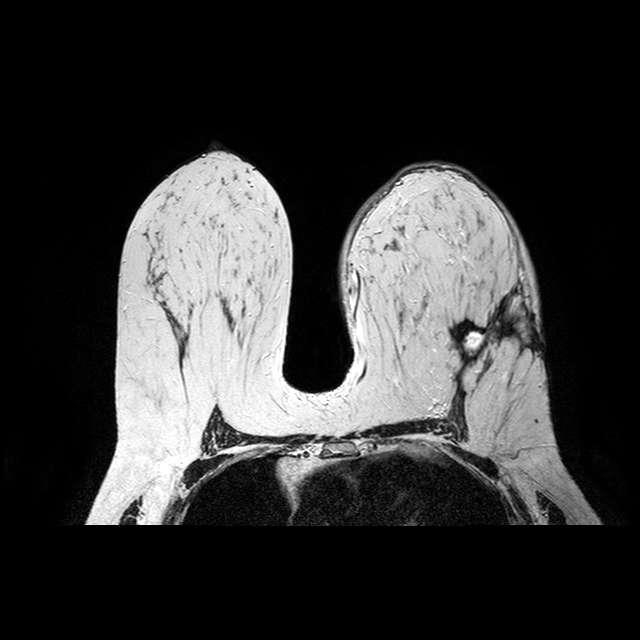
Breast MRI examination; 2 images, each one mid-volume slice chosen by position. Patient in her 40s.
Image 1: fluid-sensitive (T2/STIR) axial slice, series "T2W_TSE SENSE", slice 48 of 95.
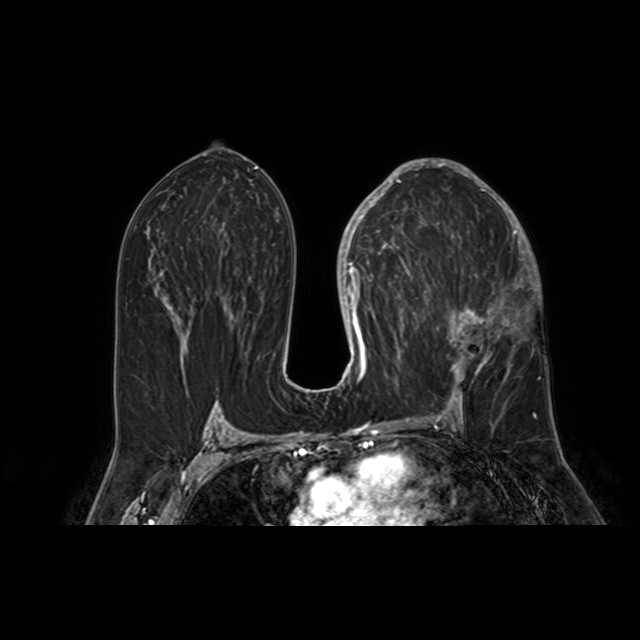
Image 2: post-contrast dynamic axial slice, slice 48 of 95, dynamic phase 5 of 8, 4 mm slice thickness.
Patient-level pathology facts (from the clinical record, not from the images): pathology diagnosis: invasive ductal CA (left breast); receptor status (as recorded): ER pos, PR pos, HER2 pos.